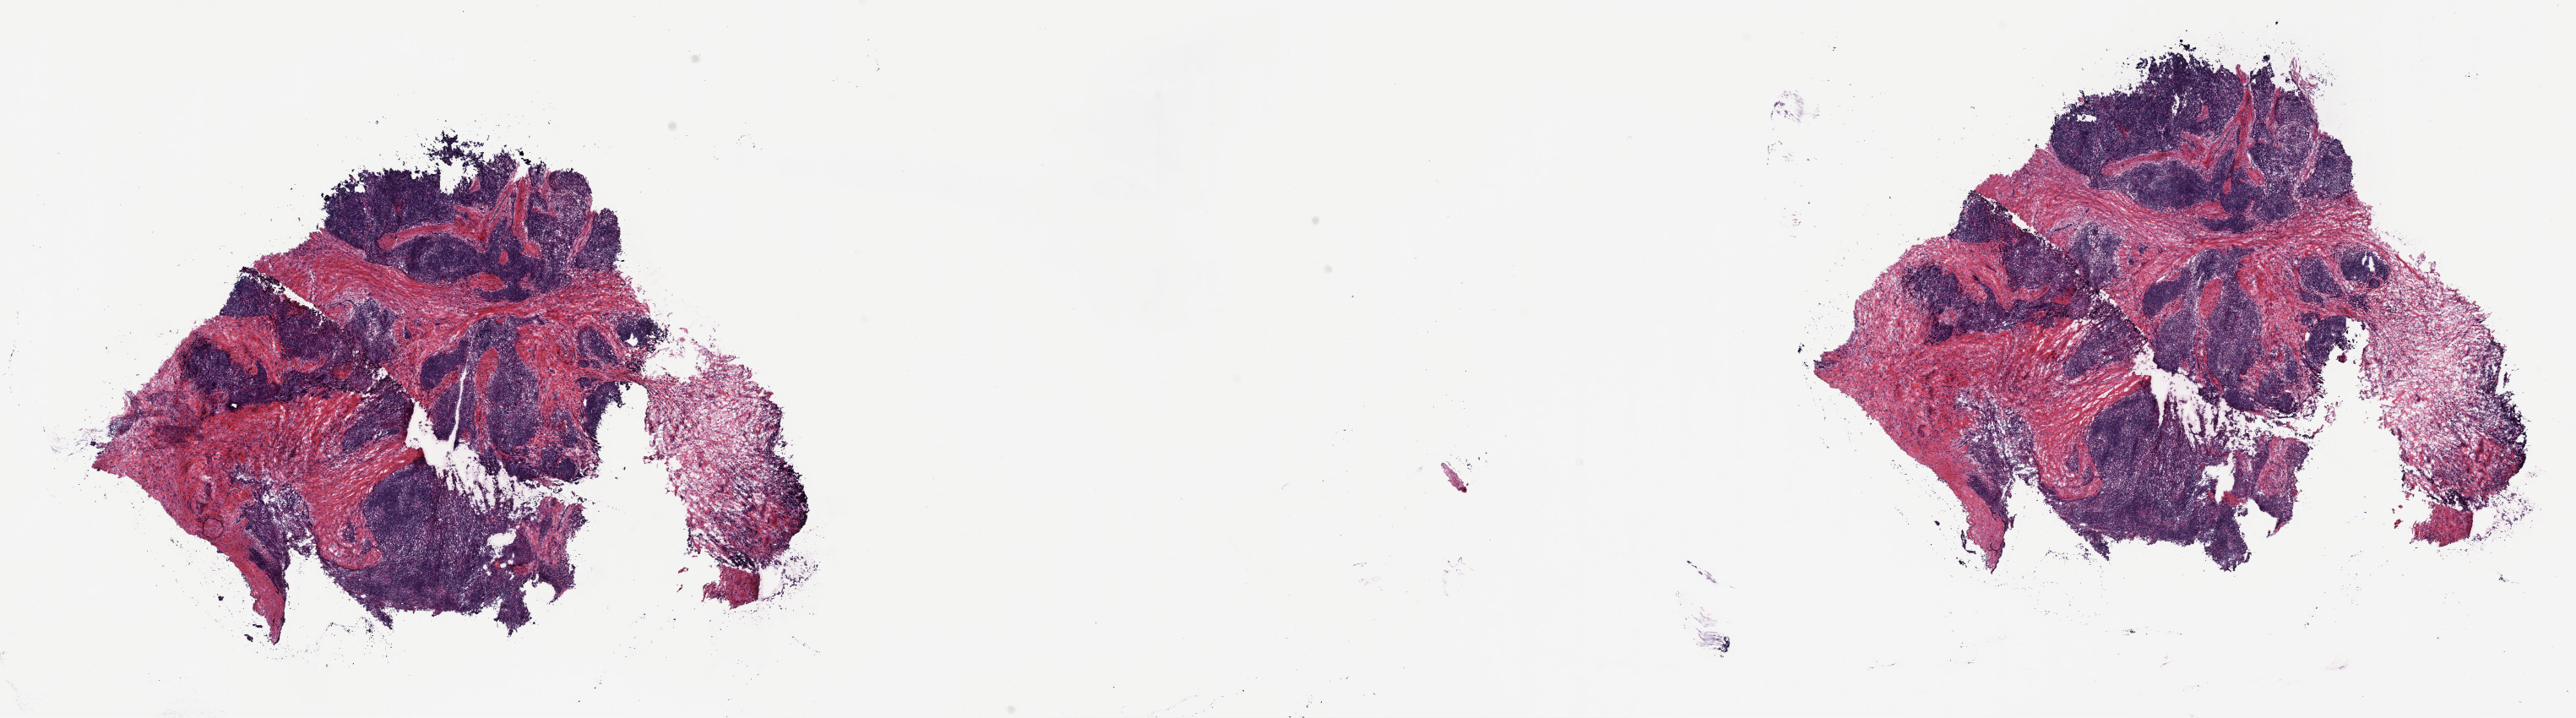
H&E-stained whole-slide image, whole scanned area (about 24.7 x 6.9 mm, slide scanned at 40x) shown as a low-resolution overview; frozen section from the top of the tissue portion; primary tumour sample from the thymus. Patient: female, age at initial diagnosis 39 years. Slide review estimates, as recorded: tumour cells 70%, tumour nuclei 70%, normal cells 0%, stromal cells 30%, necrosis 0%. Infiltration values recorded for this section: lymphocyte infiltration 2%, monocyte infiltration 1%, neutrophil infiltration 2%.
• diagnosis: Thymoma, type B2, malignant